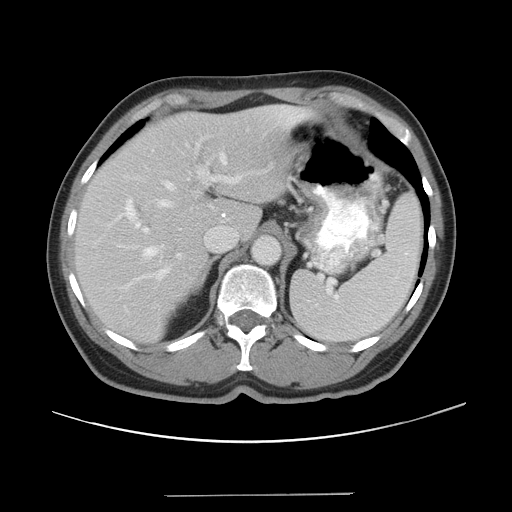
Contrast-enhanced abdominal CT, one axial slice. Position 29 of 43 along the scan axis. Reconstruction kernel STANDARD. 120 kVp. Intravenous contrast given. Soft-tissue window (W 400 / L 40 HU). 512 × 512 image matrix, field of view 409 × 409 mm. Male patient, age 65 years. From the clinical record (not read from this slice): diagnosis: colorectal cancer liver metastases, imaged before liver resection; multiple liver metastases: no; largest metastasis: 3.8 cm; chemotherapy before resection: yes.
Annotated regions visible in this slice (outlined manually by an expert reader):
- hepatic veins: box from (x=145, y=162) to (x=227, y=261) px
- liver: (x=75, y=107)–(x=296, y=342)
- planned liver remnant (the part of the liver to remain after resection): (x=75, y=107)–(x=296, y=342)
- portal vein (with intrahepatic branches): (x=116, y=138)–(x=268, y=281)